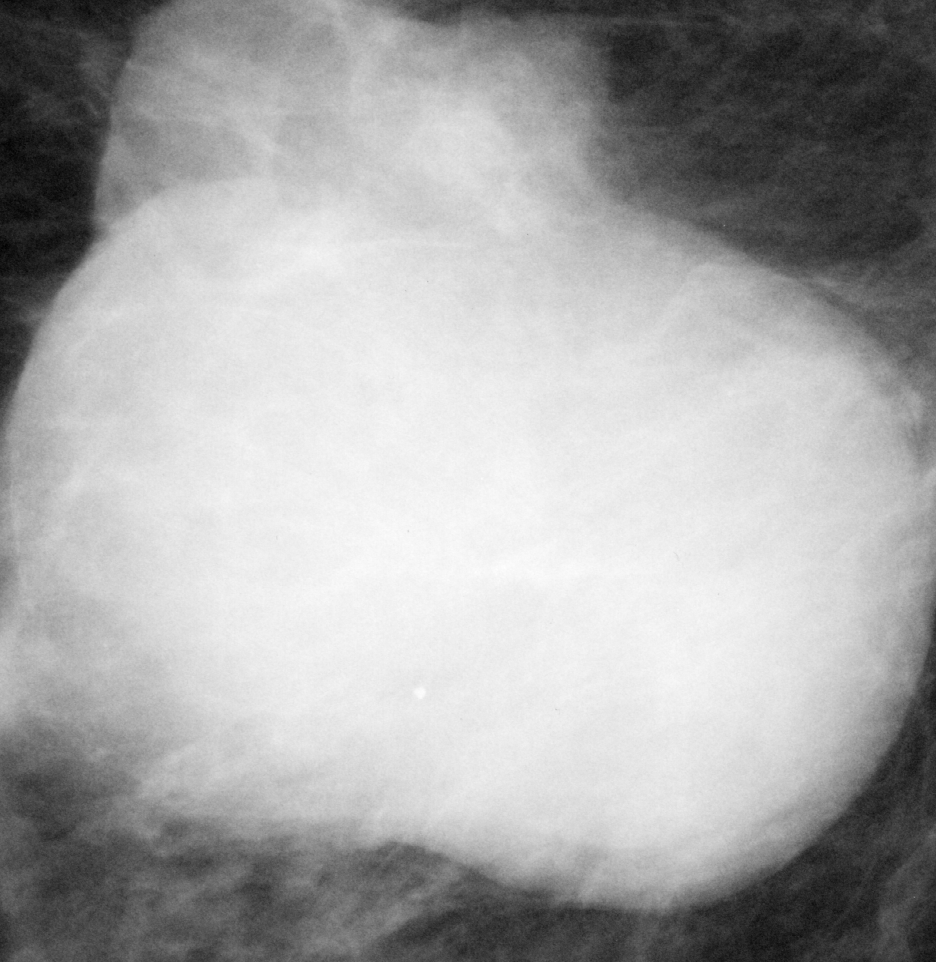
Crop from a digitized film mammogram around one marked abnormality, right breast, MLO view.
- Mass, shape lobulated, margins circumscribed; BI-RADS assessment category 5; pathology (as recorded): malignant.